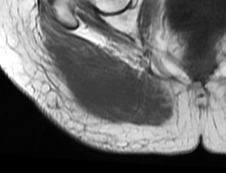
MRI of an extremity soft-tissue mass, one axial slice. Slice 27 of 73 in the series (ordered by position). MR volume resampled by the dataset authors to the PET/CT grid (not the native acquisition matrix). 3.27 mm slice thickness. 226 × 173 image matrix. Female patient. Case-level facts recorded for this patient, not image findings: histological type: spindle cell suggestive of myxofibrosarcoma; grade: intermediate; site of the primary tumour: right buttock.
Structures marked on this image (expert contour drawn on MRI and transferred to this co-registered scan by the dataset authors):
- gross tumour volume (mass): box from (x=45, y=40) to (x=142, y=114) px